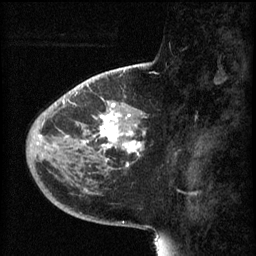
Breast MRI (dynamic contrast-enhanced), one sagittal slice. Slice 21 of 60 in the series (ordered by position). 3 images stored at this slice position (order not interpretable as contrast timing). 1.5 T. TE 4.2 ms, TR 8.1 ms. 2 mm slice thickness. 256 × 256 image matrix, field of view 200 × 200 mm. Patient: female, 44 years.
Structures marked on this image (semi-automatic segmentation, software-assisted and operator-edited):
- analysis volume of interest (the breast-tissue region the enhancement analysis was run in; not a lesion): bounding box (x1, y1, x2, y2) in pixels: (59, 110, 146, 169)
- tumour enhancement mask (voxels above the 70 % enhancement threshold inside the analysis volume of interest): (83, 110, 145, 167)